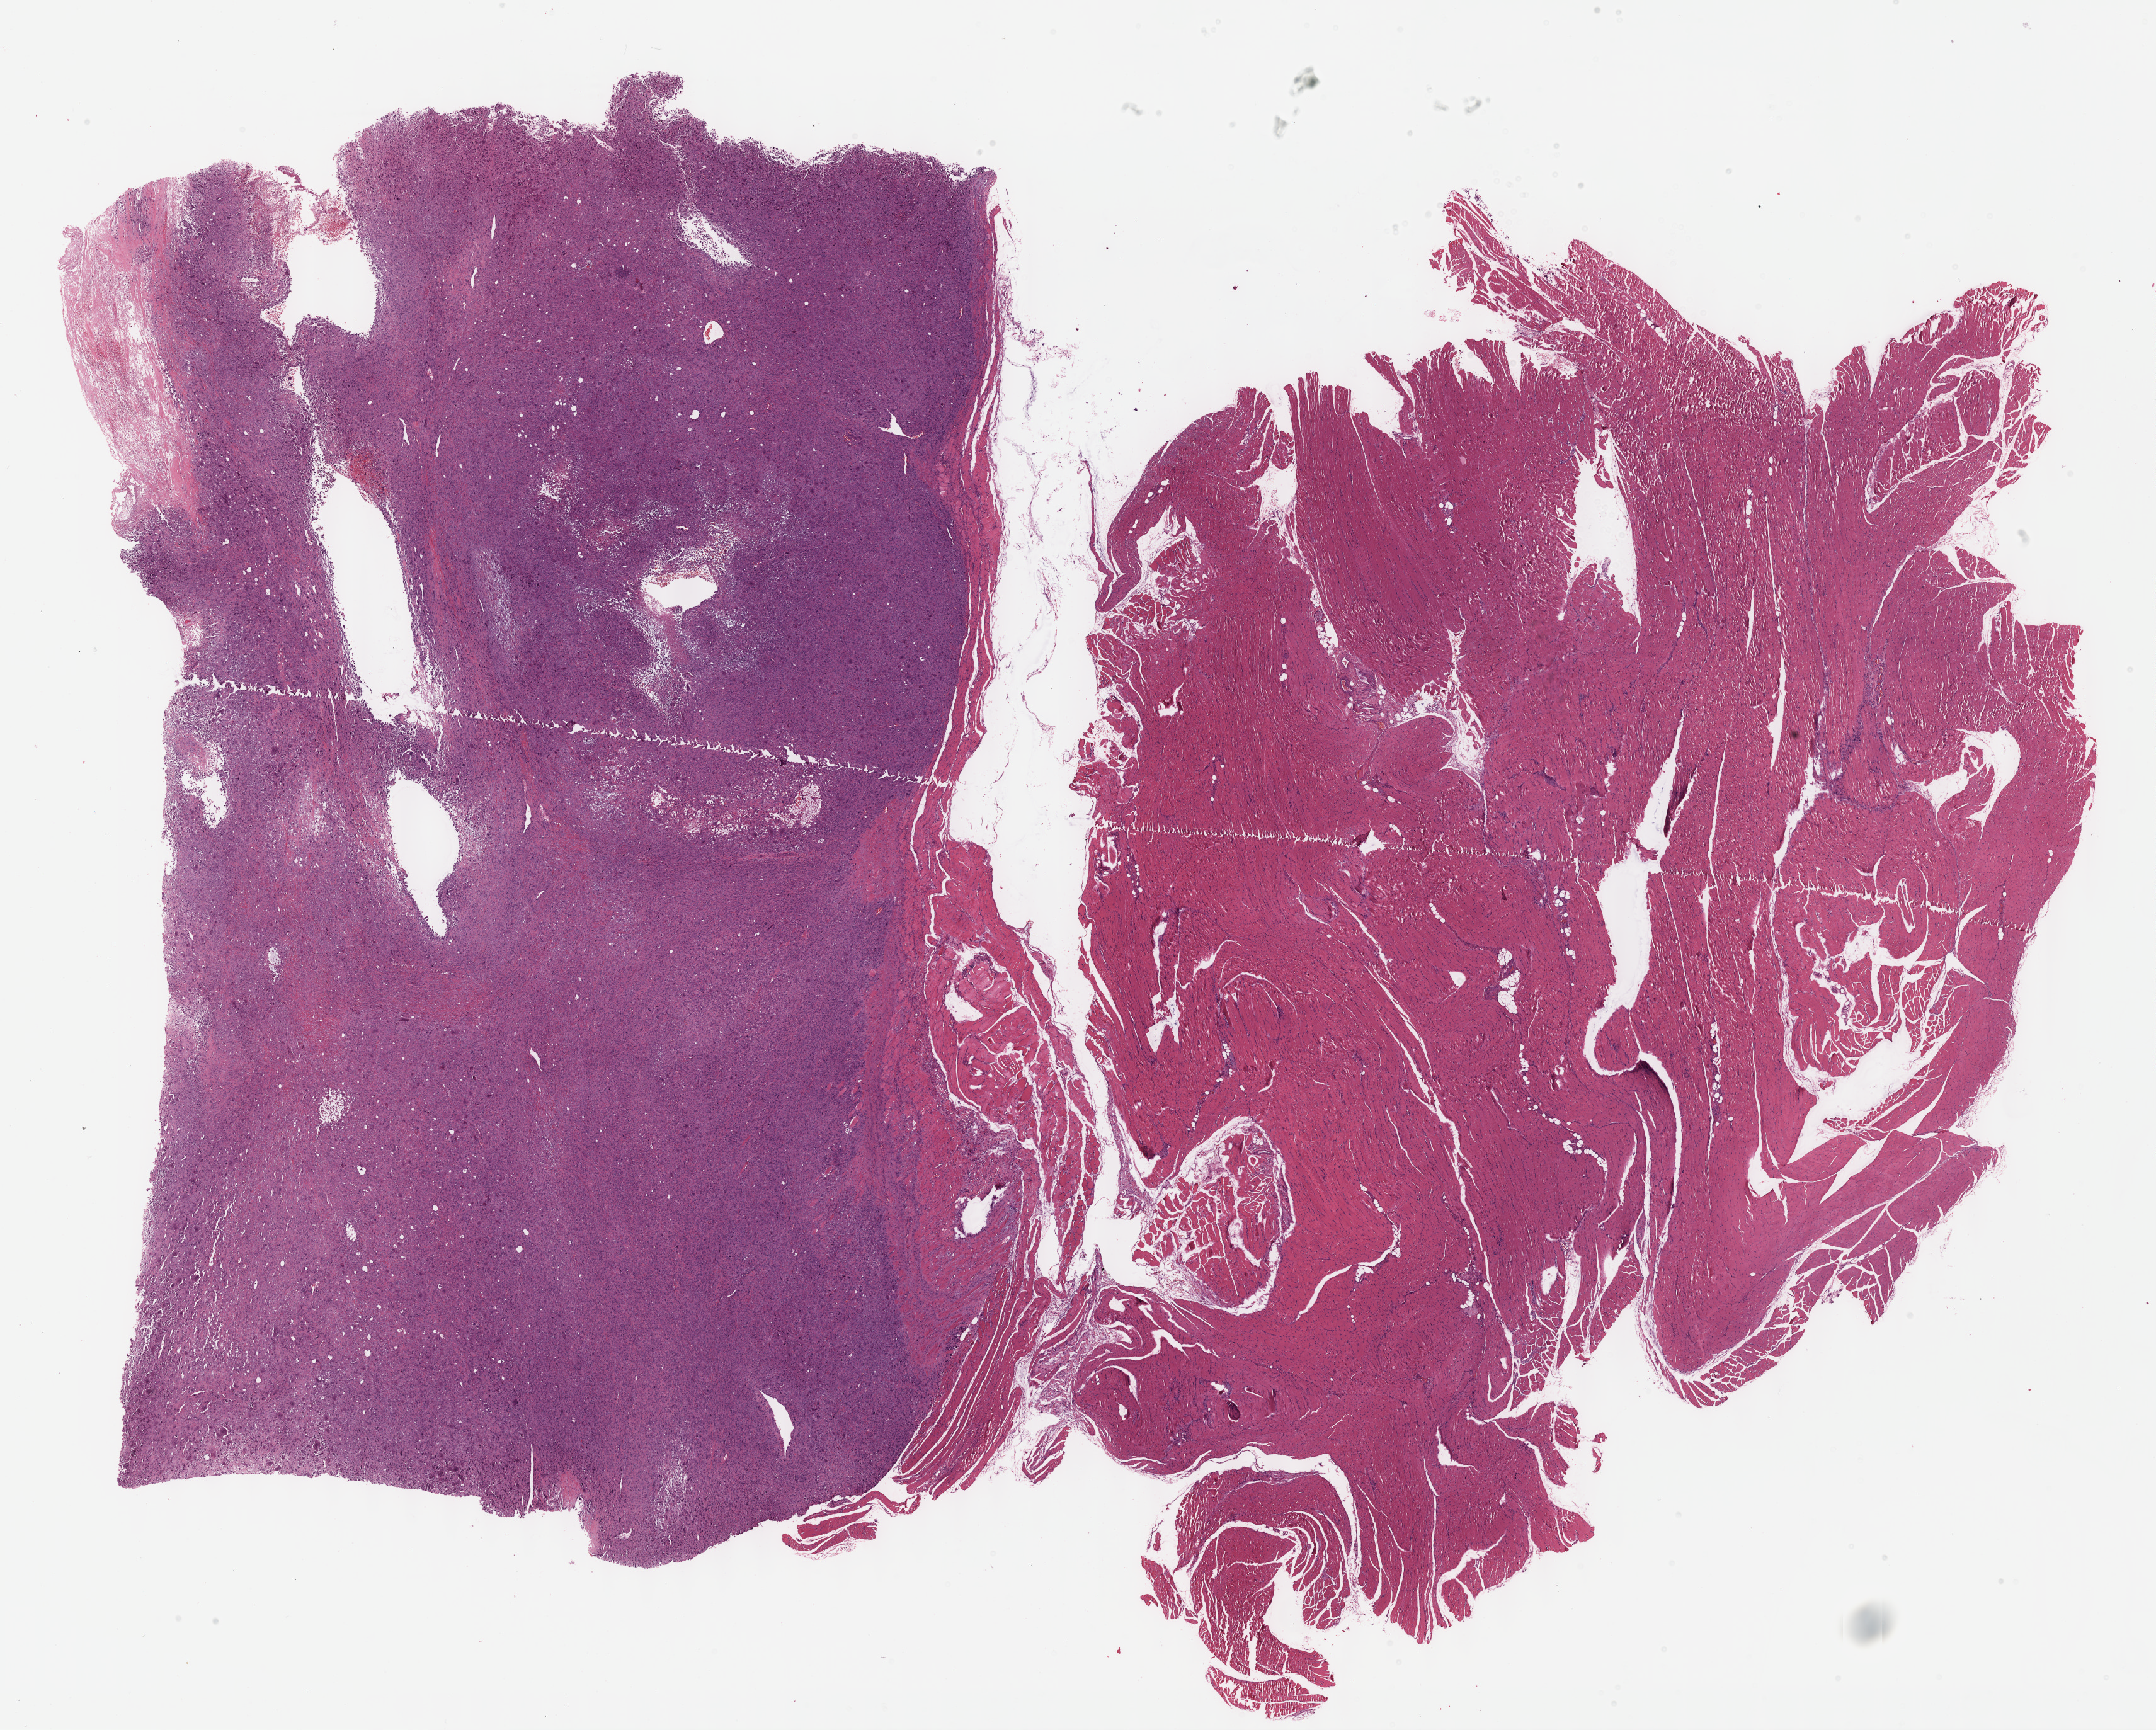
H&E whole-slide image, low-resolution overview of the scanned area, about 27.7 x 22.2 mm (from a 40x scan). FFPE section. Connective, subcutaneous and other soft tissues, primary tumour sample. Female patient.
Pathologic diagnosis: Undifferentiated sarcoma (connective, subcutaneous and other soft tissues of lower limb and hip).